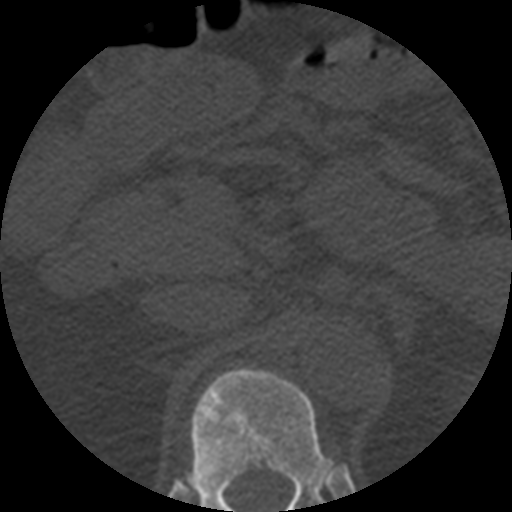
CT including the spine, one axial slice; position 214 of 508 along the scan axis; bone window (W 1800 / L 400 HU); 1.25 mm slice thickness; 512 × 512 image matrix, field of view 160 × 160 mm. Patient age 57 years. From the clinical record (not read from this slice): primary cancer: prostate.
Outlined on this slice (semi-automatically segmented with operator editing):
- T12 vertebra: box from (x=180, y=368) to (x=350, y=512) px